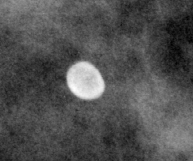
Cropped region of a digitized screen-film mammogram centred on a radiologist-marked abnormality, right breast, CC view, BI-RADS breast density category 3 (scale 1–4).
Calcifications, morphology lucent center; BI-RADS assessment category 2; subtlety rating 5 on a 1 (subtle) to 5 (obvious) scale; benign; no additional work-up was recommended (benign without callback).